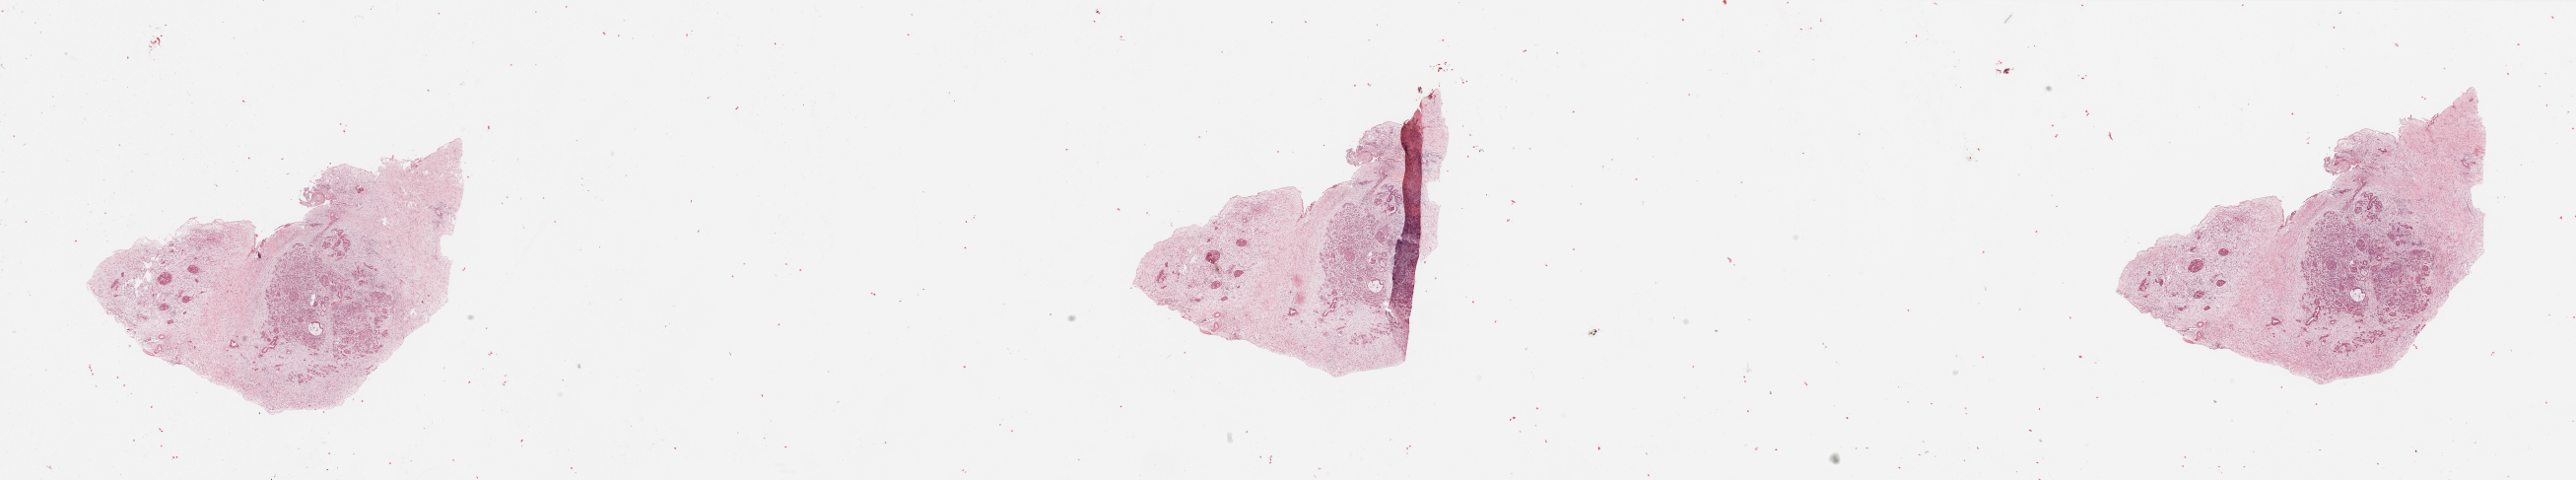
Hematoxylin and eosin (H&E) stained whole-slide image — a low-resolution overview of the entire scanned area, about 41.3 x 7.7 mm, pancreas, normal (non-tumour) tissue. 64-year-old female patient.
This section: normal (non-tumour) tissue from the same patient. Patient diagnosis: Infiltrating duct carcinoma, NOS.